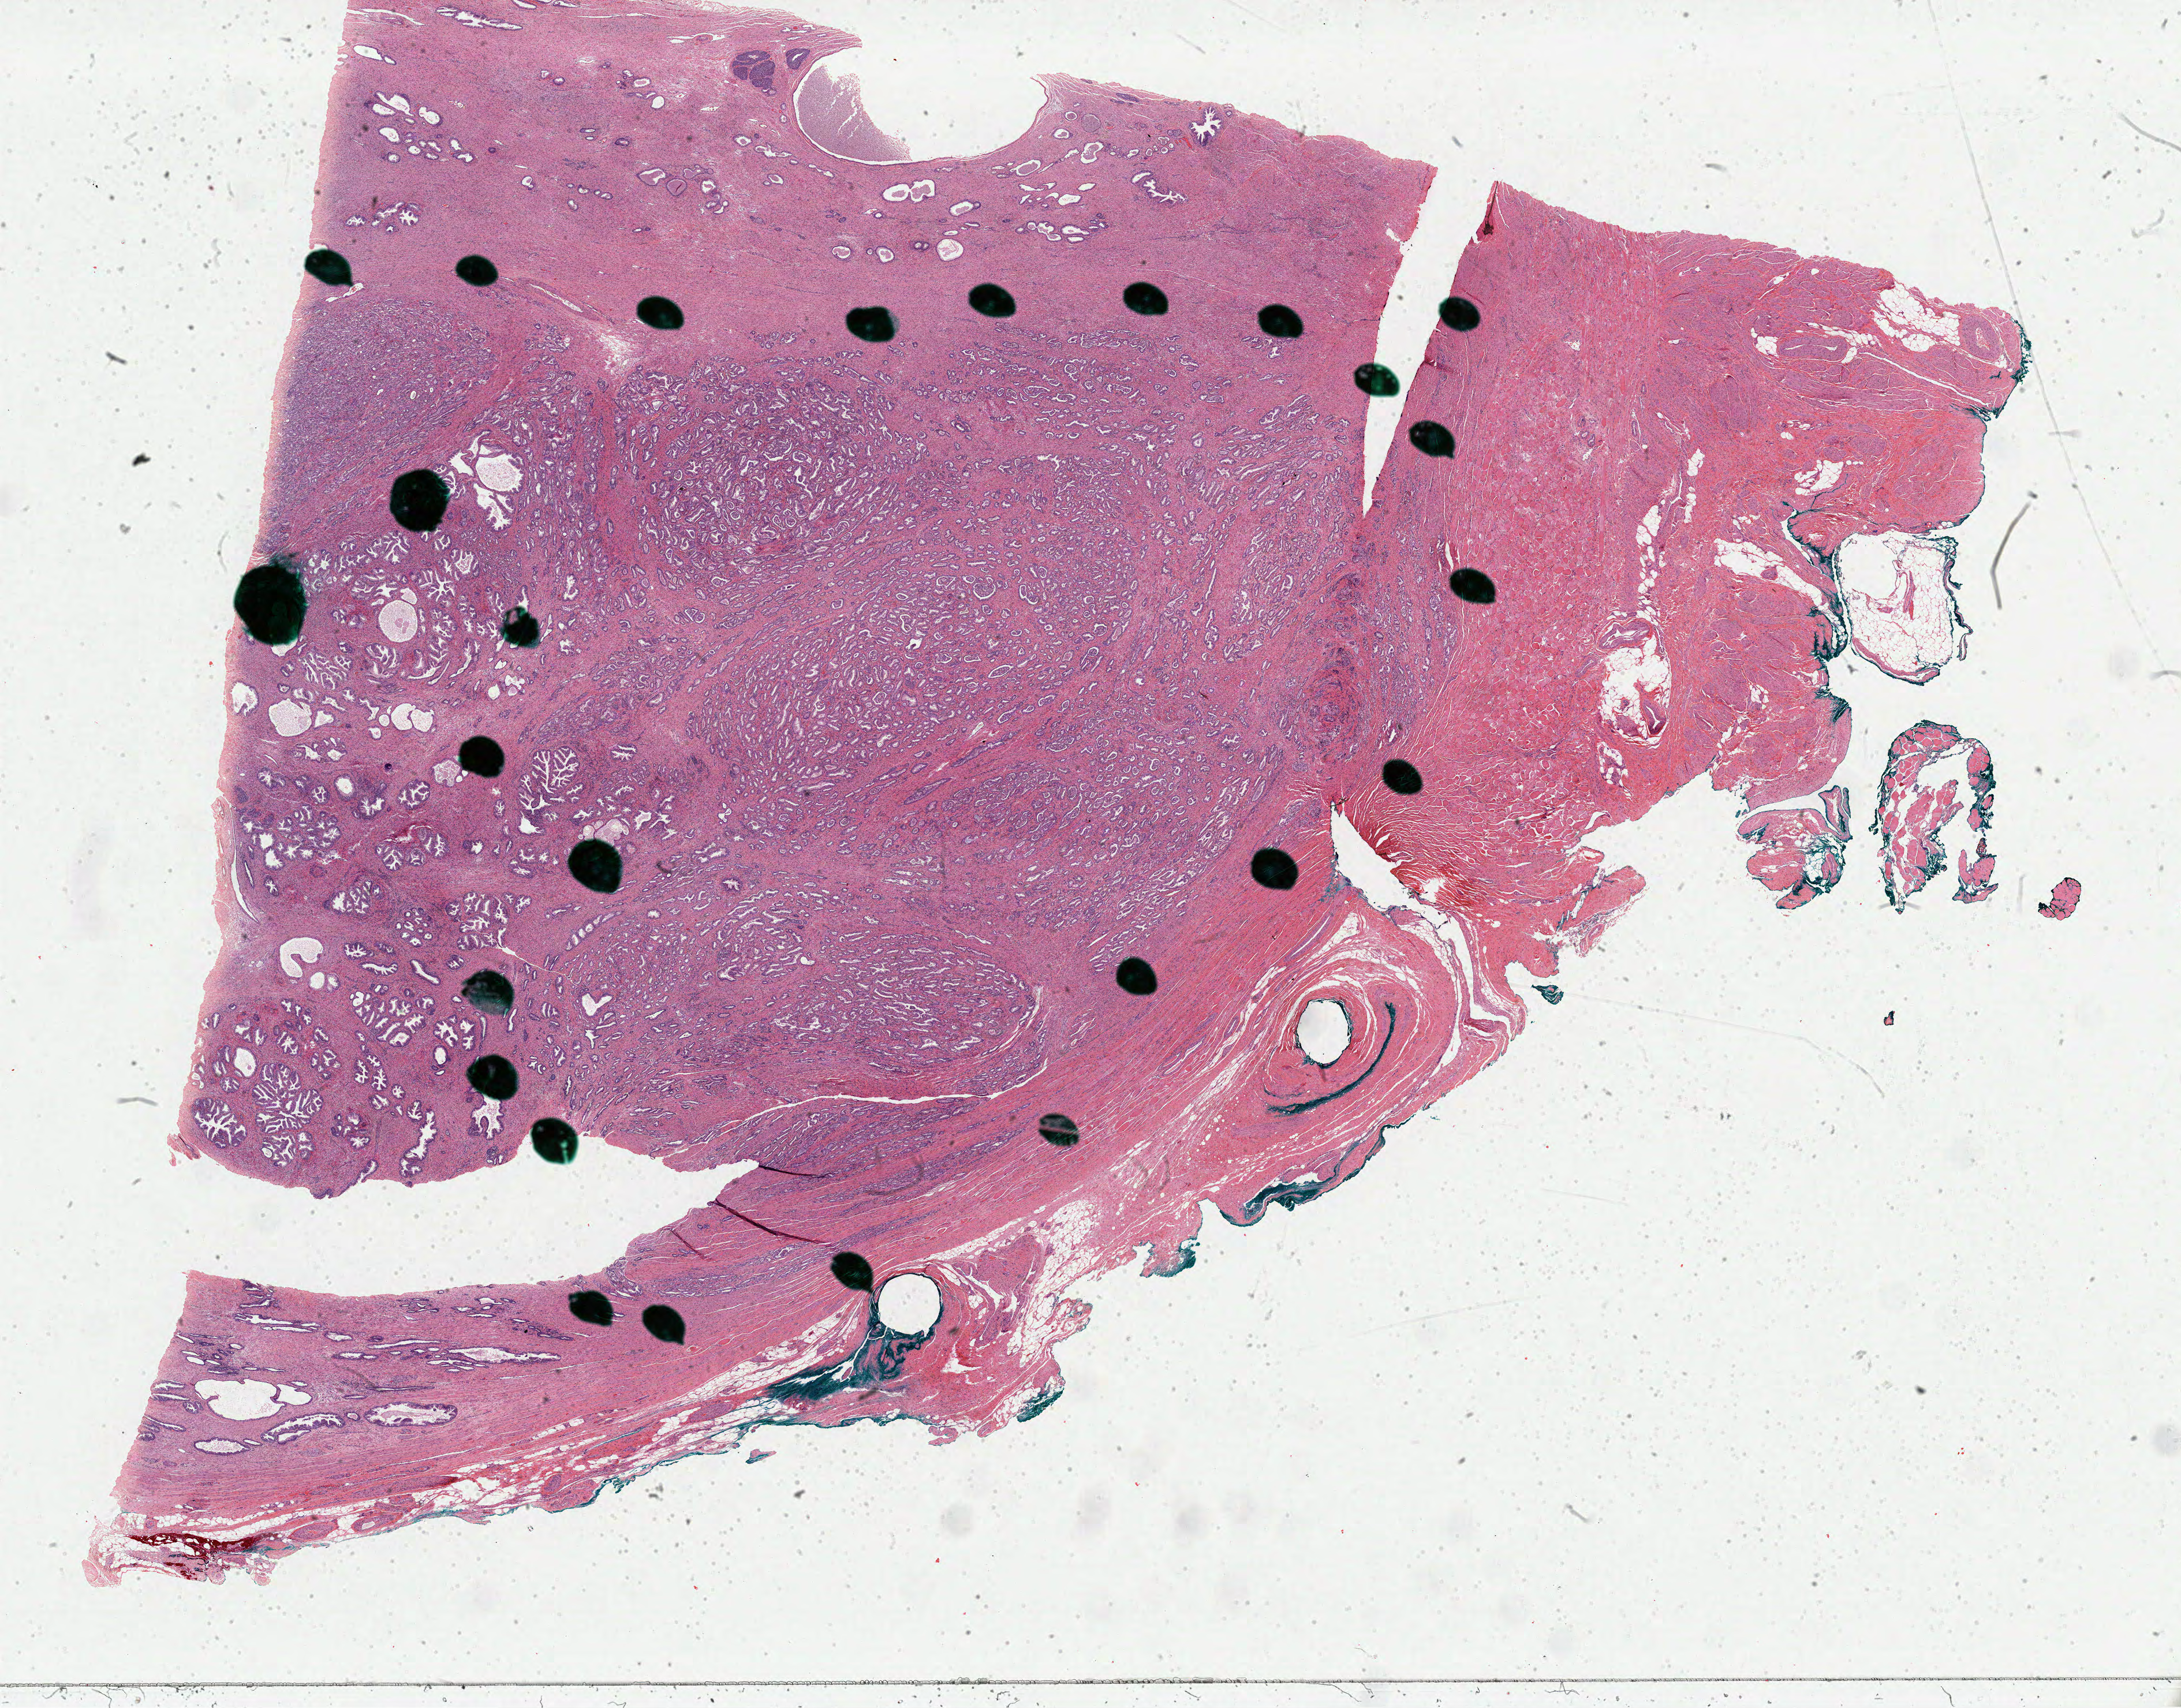
H&E whole-slide image, low-resolution overview of the scanned area, about 29.8 x 23.4 mm. Formalin-fixed paraffin-embedded (FFPE) diagnostic section. Prostate, primary tumour sample. Male, age 56 years at initial diagnosis. Gleason score: 7 (3+4).
Lymph nodes positive (case pathology): 0 of 3 examined. Pathologic diagnosis: Adenocarcinoma, NOS (prostate gland).